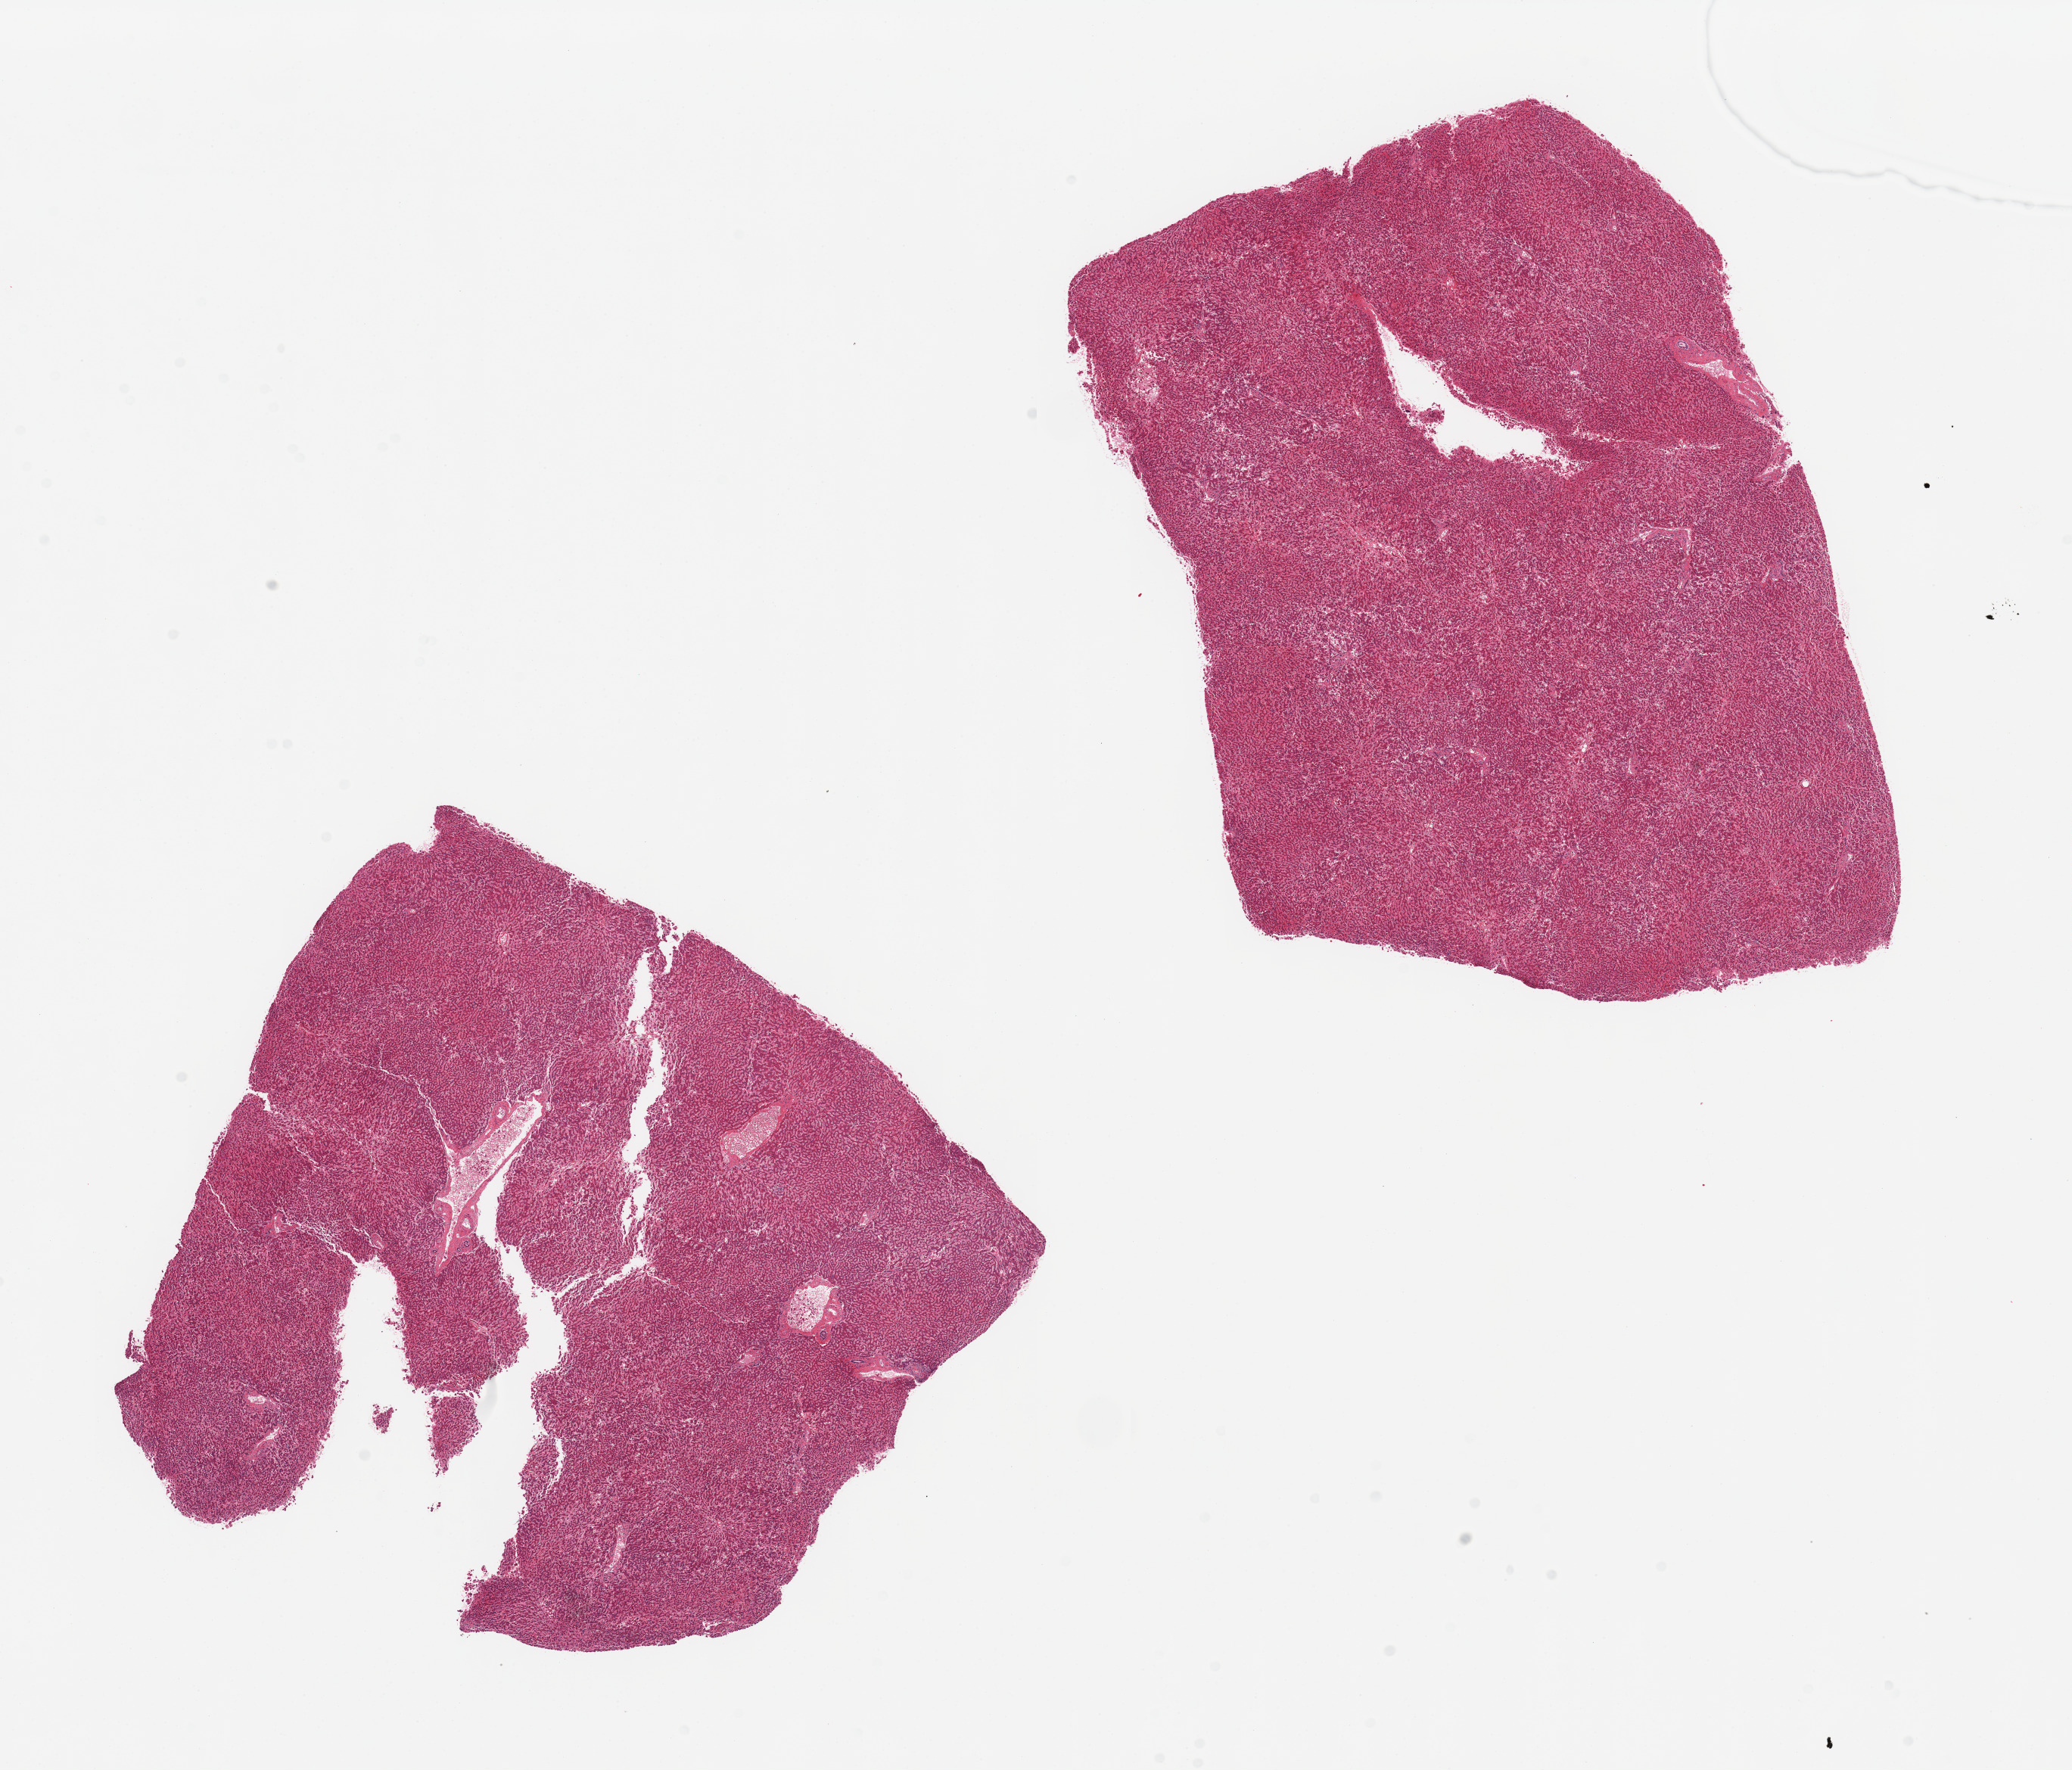
H&E whole-slide image, a low-resolution overview of the entire scanned area, about 21.7 x 18.5 mm, PAXgene-fixed paraffin-embedded (PFPE) section, section of liver (target tissue), tissue donor sample. Female donor.
Reviewer comment on this tissue sample: 2 pieces, mild congestion, minimal steatosis.